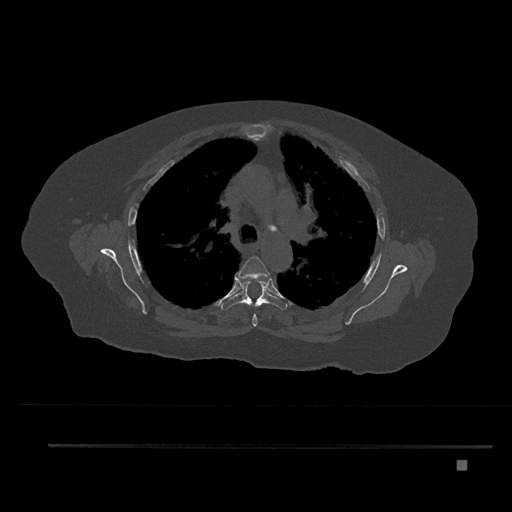
CT including the spine, one axial slice; position 580 of 797 along the scan axis; reconstruction kernel Br40s/3; 120 kVp; bone window (W 1800 / L 400 HU); 0.5 mm slice thickness; 512 × 512 image matrix, field of view 437 × 437 mm. Female patient, age 76 years. Case-level facts recorded for this patient, not image findings: primary cancer: lung; vertebrae with lytic lesions (as recorded): T11, L3.
Annotated regions visible in this slice (semi-automatic segmentation, software-assisted and operator-edited):
- T4 vertebra: bounding box <235,256,270,326> (left, top, right, bottom; pixels)
- T5 vertebra: <220,278,287,310>